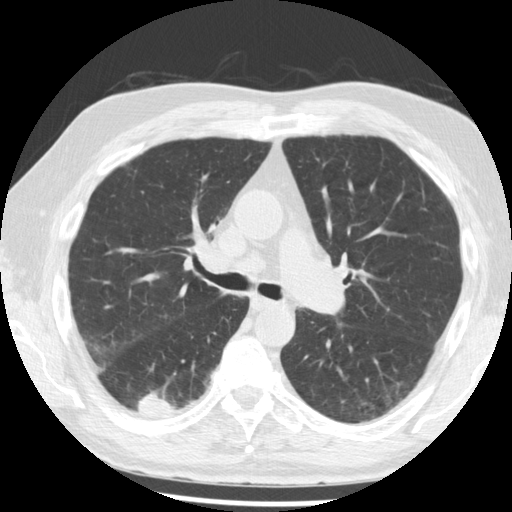
Chest CT (low-dose screening protocol), one axial image; third screening round (two years after baseline); lung window (W 1500 / L -600 HU); 2.5 mm slice thickness; standard (soft-tissue) reconstruction kernel (STANDARD); 120 kVp; 512 × 512 image matrix, field of view 350 × 350 mm. Male participant, aged 68 years at enrolment. Current smoker at enrolment.
Lesion marked by an expert reader, bounding box <121,378,189,428> (left, top, right, bottom; pixels). The screening reader recorded 3 non-calcified nodules or masses ≥4 mm on this exam (right lower lobe, right lower lobe, right lower lobe); which of them this box marks is not recorded. Participant outcome: lung cancer diagnosed 48 days after this screen — squamous cell carcinoma, NOS, right lower lobe, moderately differentiated (G2), stage IB (AJCC 6th edition), 20 mm at pathology.